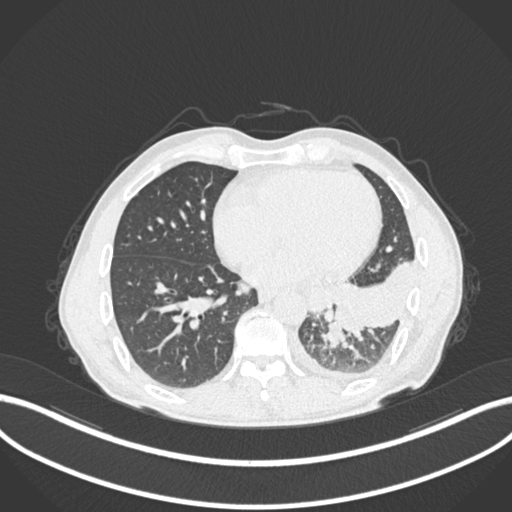
Chest CT, one axial slice. Position 87 of 222 along the scan axis. Reconstruction kernel B30f. Lung window (W 1500 / L -600 HU). 512 × 512 image matrix. Patient: male, 47 years. Case-level facts recorded for this patient, not image findings: clinical TNM (as recorded): T3 N1 M1c.
Annotated regions visible in this slice (bounding box drawn by a radiologist):
- lung tumour (recorded histology: small cell carcinoma): bounding box (x1, y1, x2, y2) in pixels: (320, 322, 349, 352)